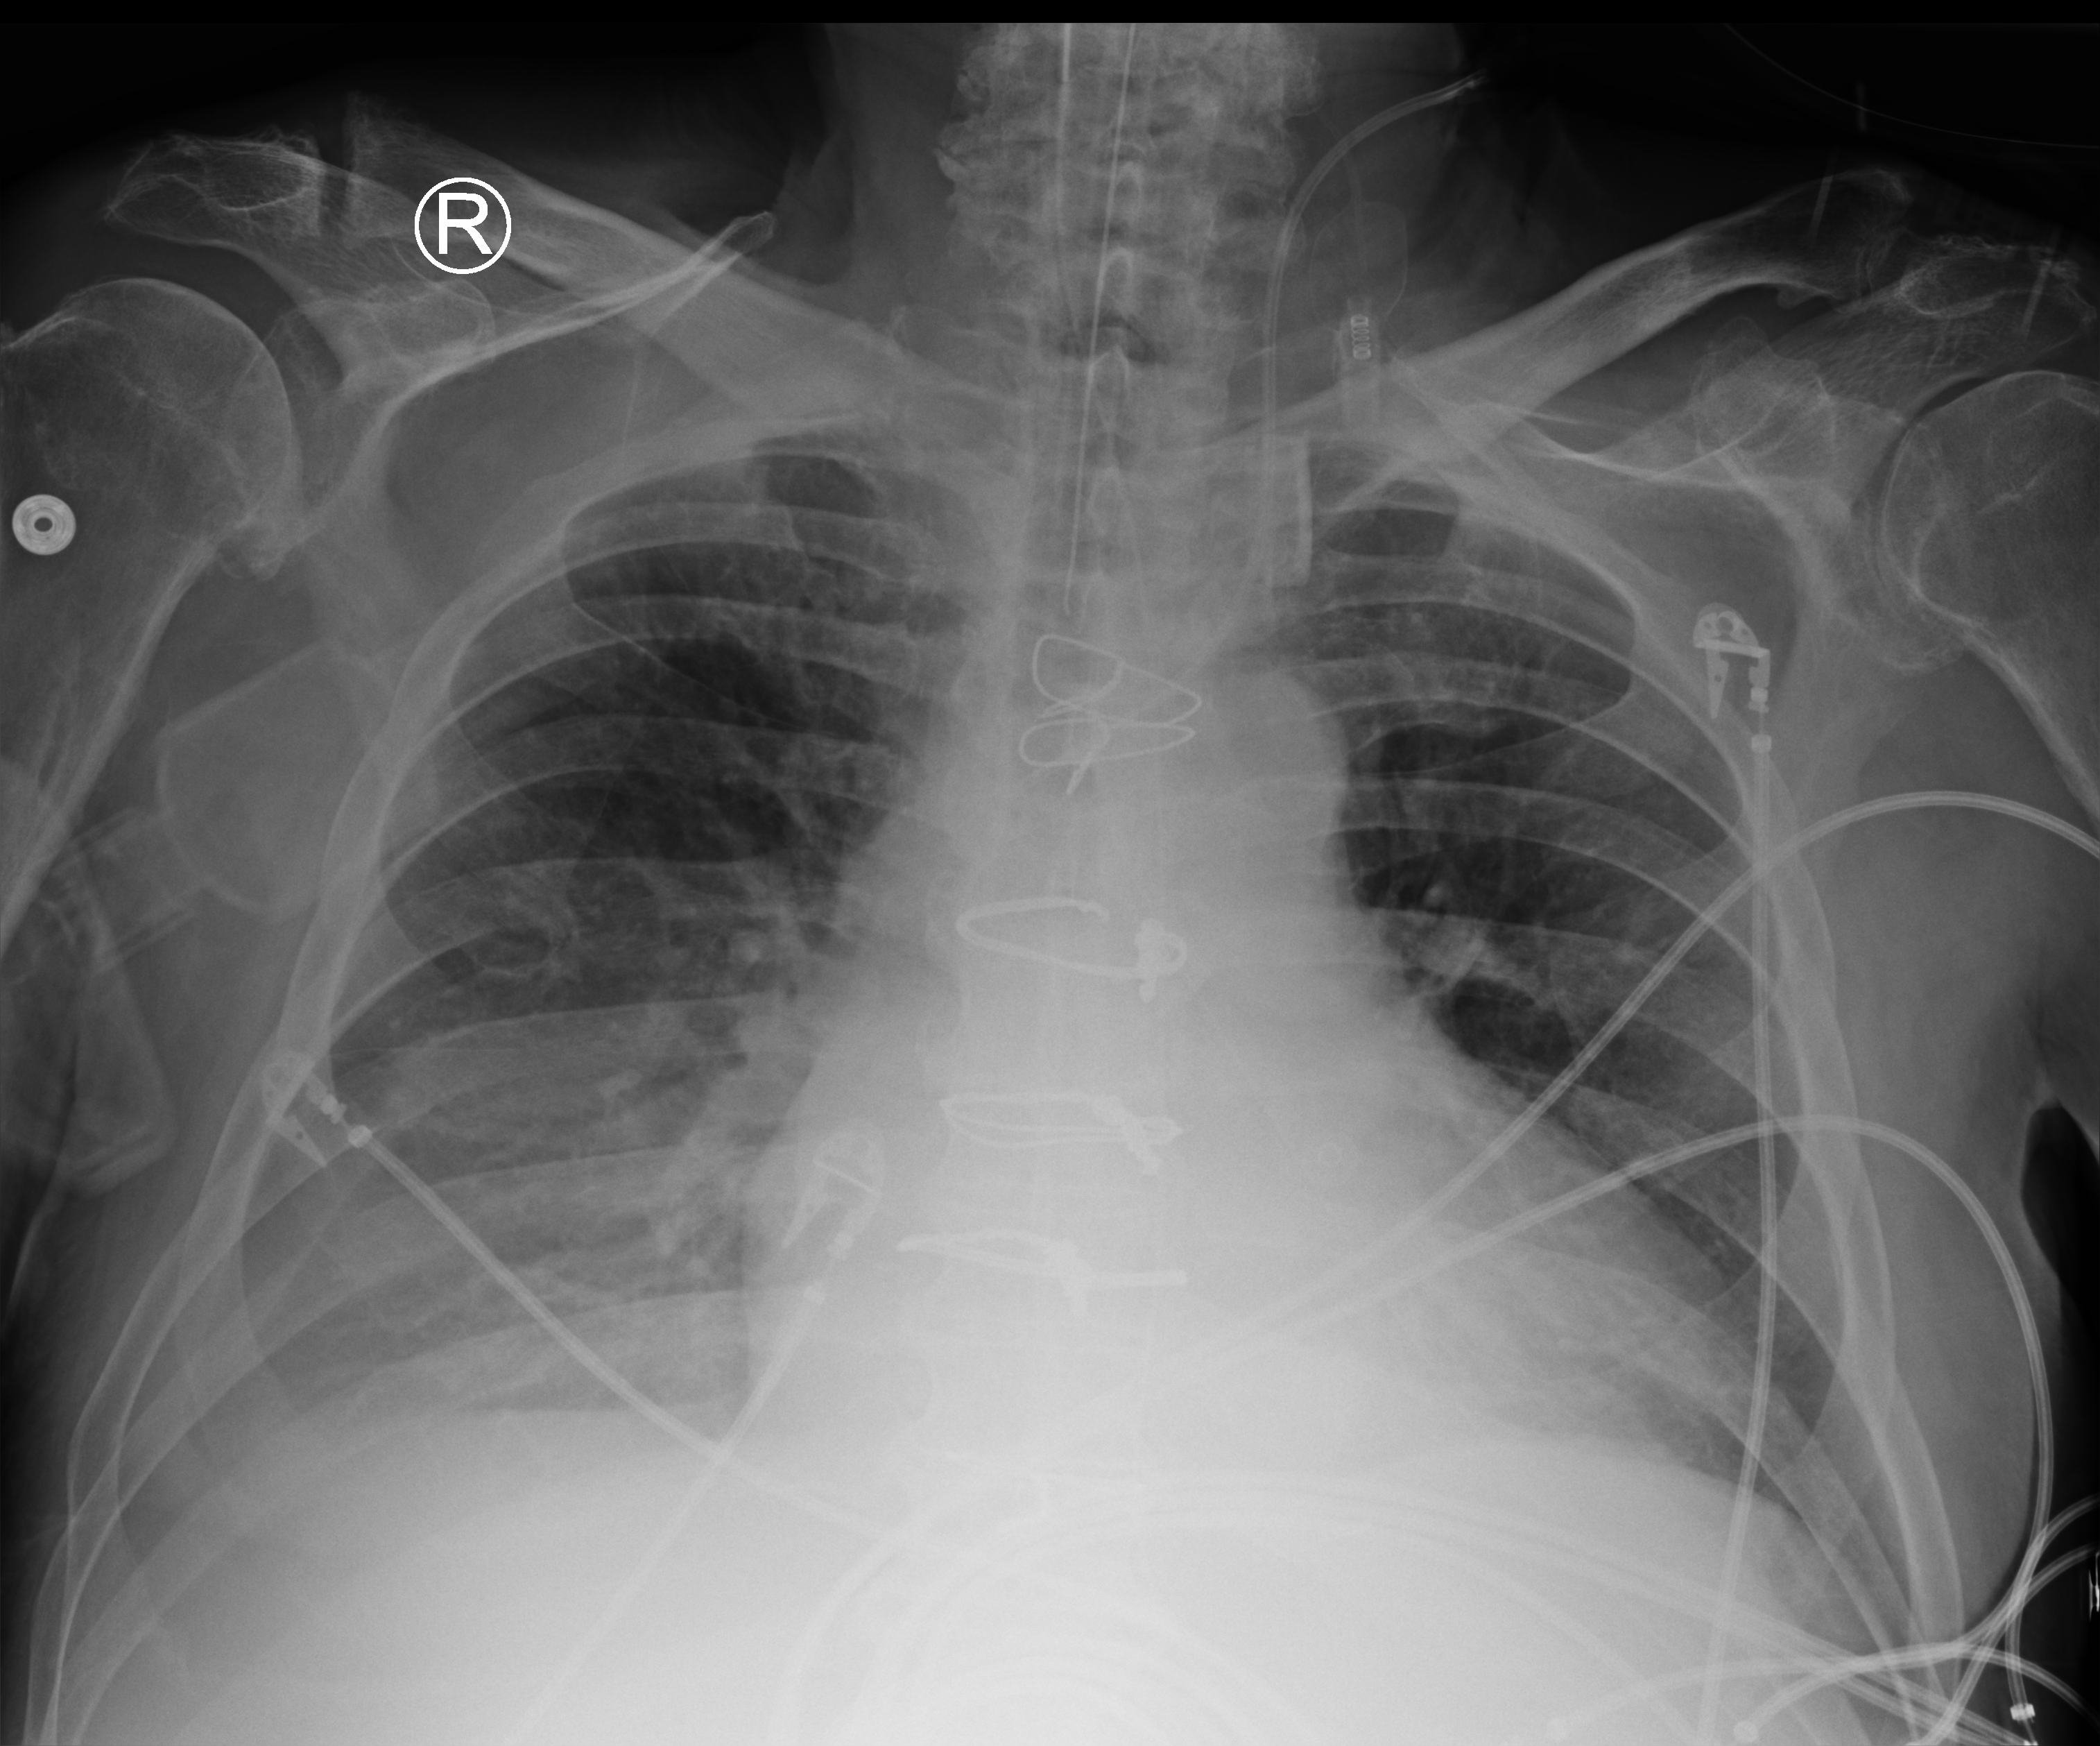
Portable chest radiograph. Patient hospitalised with COVID-19; male, aged 60–74 years.
From the hospital-stay record, not from the radiograph (when in the stay this image was taken is not recorded):
- admitted to intensive care during this hospital stay: yes
- hypertension (admission record): yes